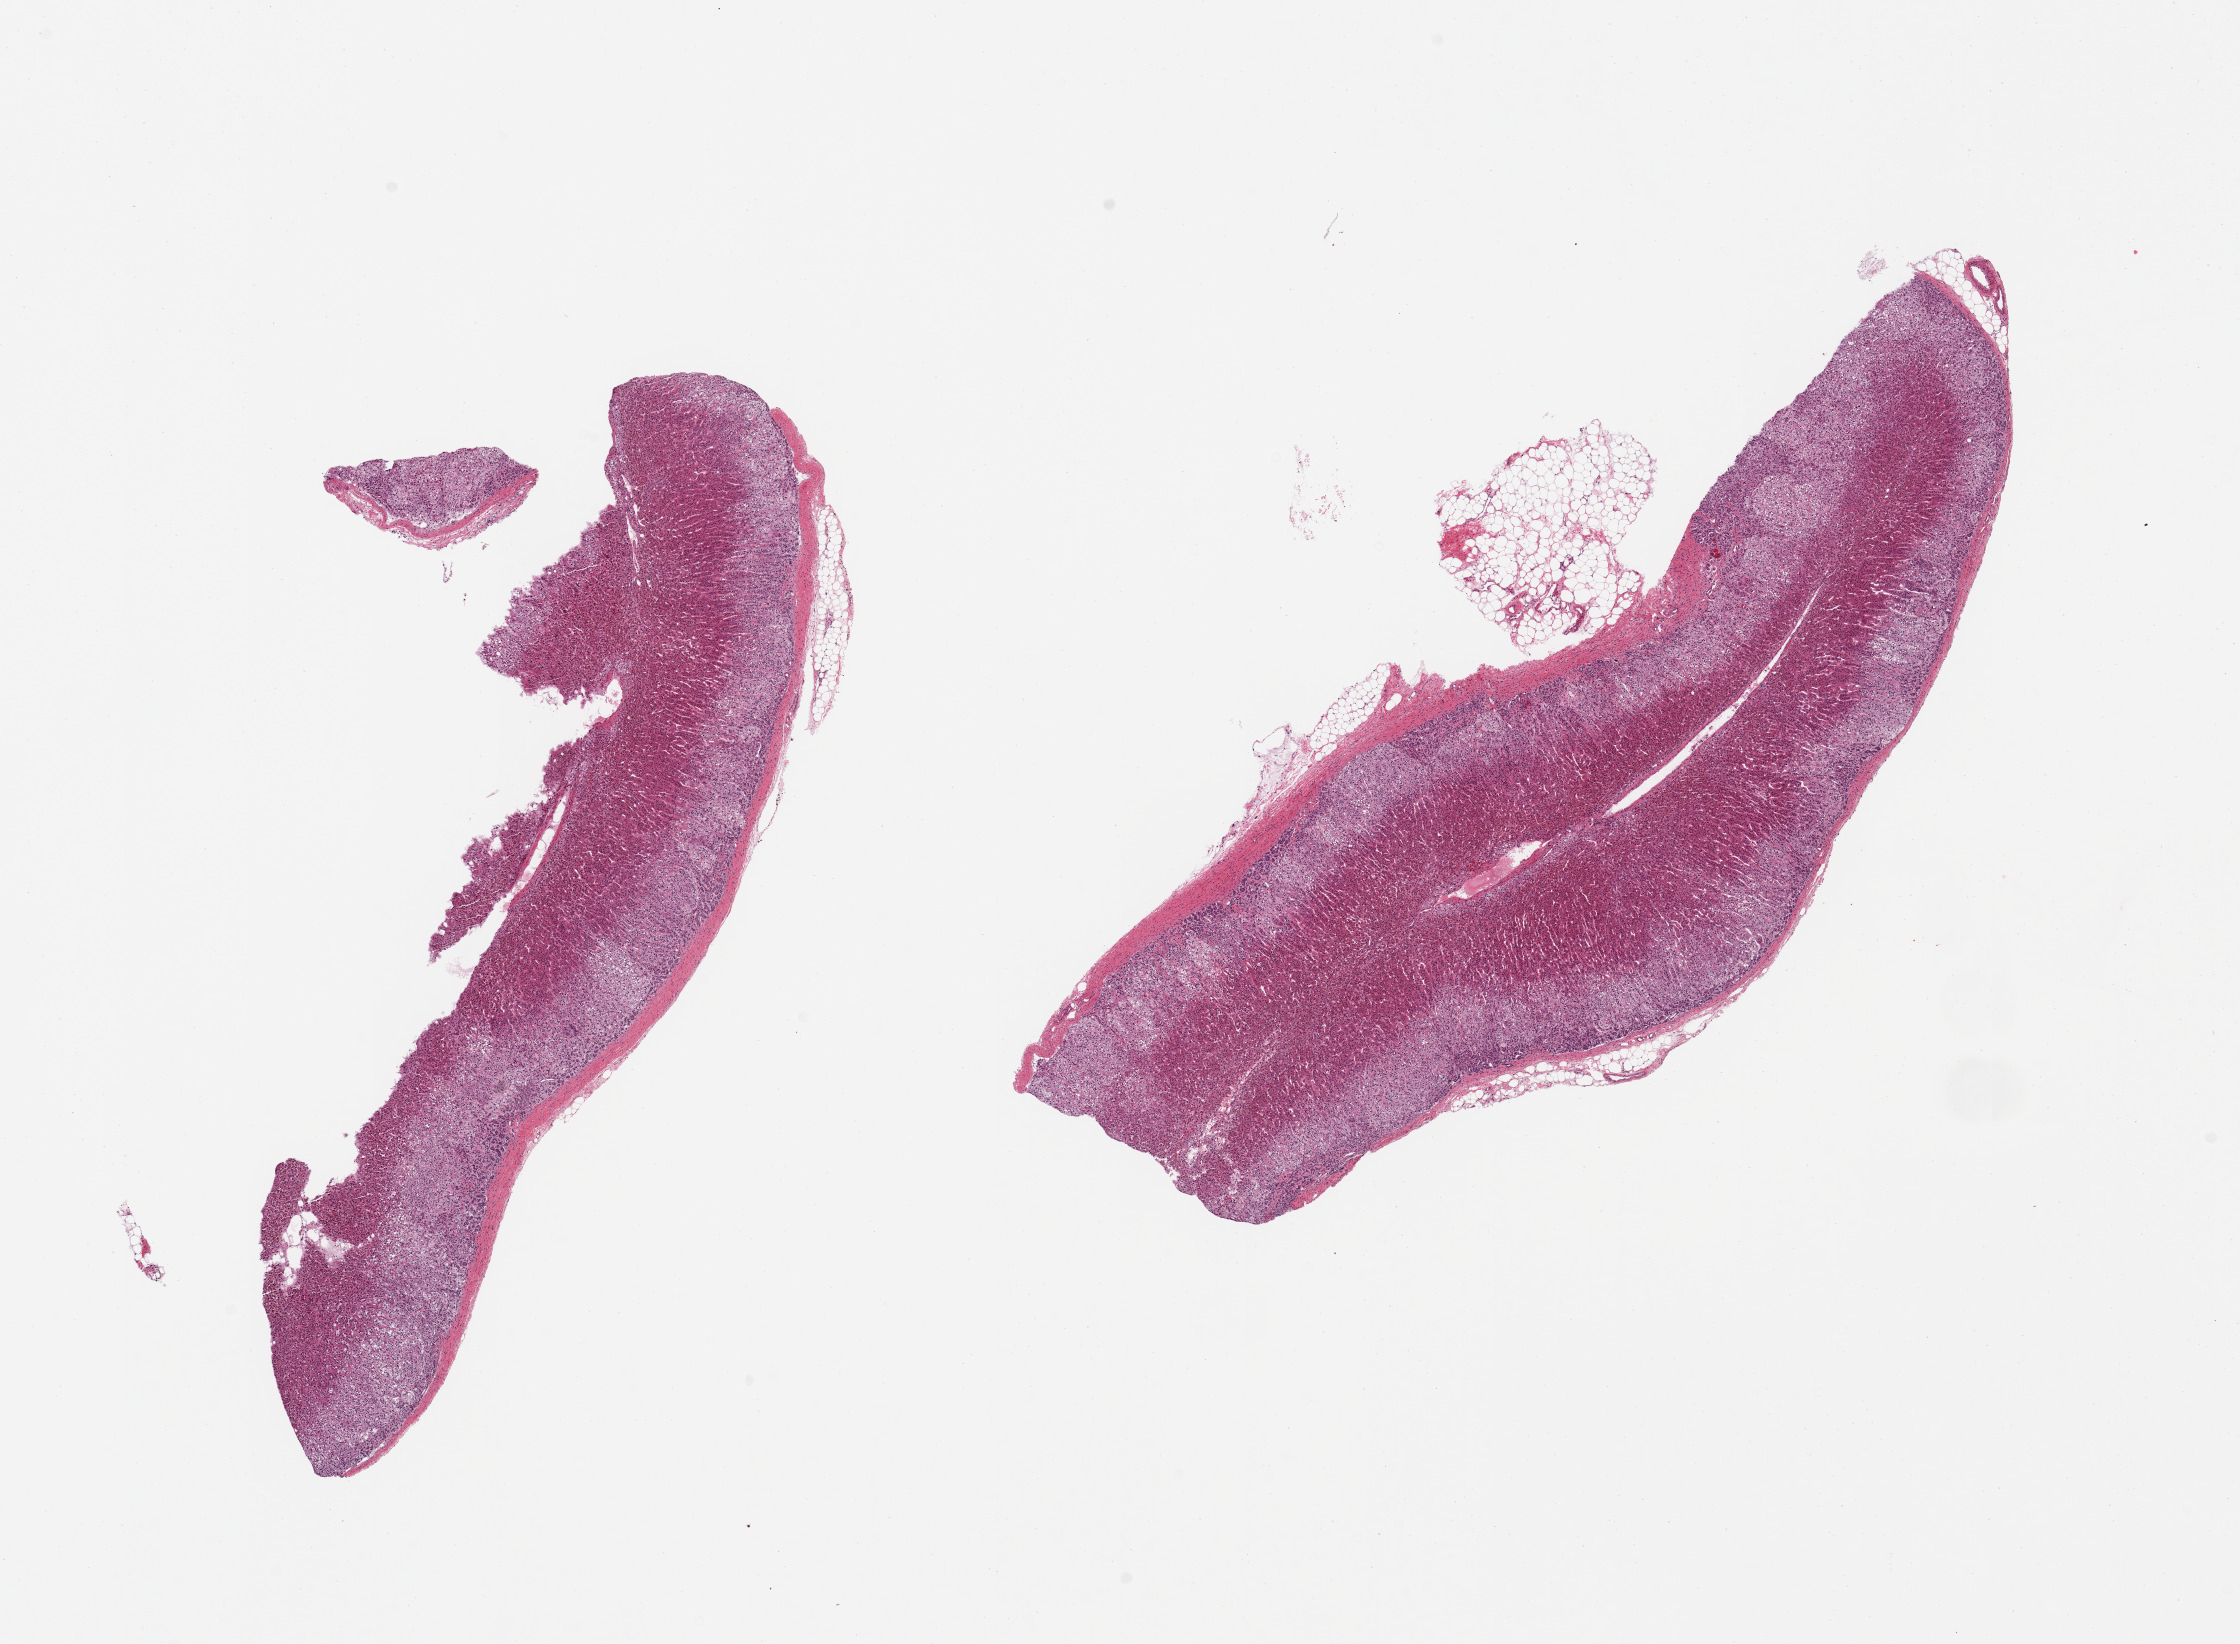
Whole-slide image, haematoxylin and eosin stain, shown as a low-resolution overview of the whole scanned area (about 17.7 x 13.0 mm); PAXgene-fixed paraffin-embedded (PFPE) section; target tissue: adrenal gland; tissue donor sample. Donor sex: female.
Reviewer comment on this tissue sample: 2 pieces; small attachment of fat.